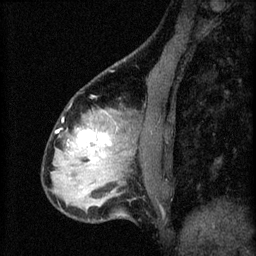
Breast MRI (dynamic contrast-enhanced), one sagittal slice. Position 22 of 60 along the scan axis. 3 images stored at this slice position (order not interpretable as contrast timing). 1.5 T. TE 4.2 ms, TR 8.2 ms. 2.3 mm slice thickness. 256 × 256 image matrix, field of view 180 × 180 mm. Female patient, age 37 years.
Outlined on this slice (semi-automatically segmented with operator editing):
- analysis volume of interest (the breast-tissue region the enhancement analysis was run in; not a lesion): bounding box (x1, y1, x2, y2) in pixels: (67, 120, 122, 179)
- tumour enhancement mask (voxels above the 70 % enhancement threshold inside the analysis volume of interest): (78, 130, 111, 161)